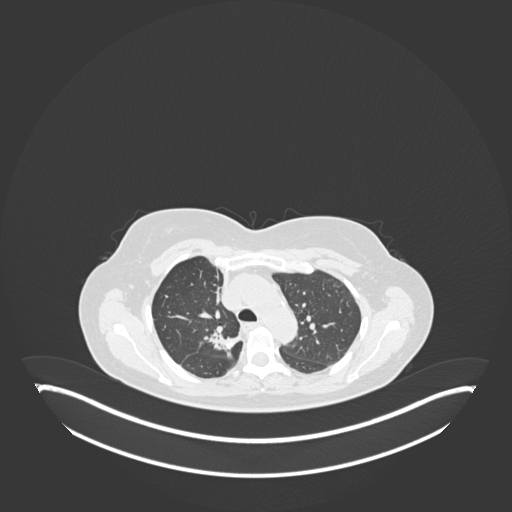
Chest CT, one axial slice; position 127 of 181 along the scan axis; reconstruction kernel B30f; 120 kVp; lung window (W 1500 / L -600 HU); 1 mm slice thickness; 512 × 512 image matrix, field of view 500 × 500 mm. Female patient, age 65 years. Case-level facts recorded for this patient, not image findings: clinical TNM (as recorded): T1b N0 M0.
Outlined on this slice (rectangle marked by the reading radiologist):
- lung tumour (recorded histology: adenocarcinoma): box from (x=204, y=328) to (x=240, y=359) px